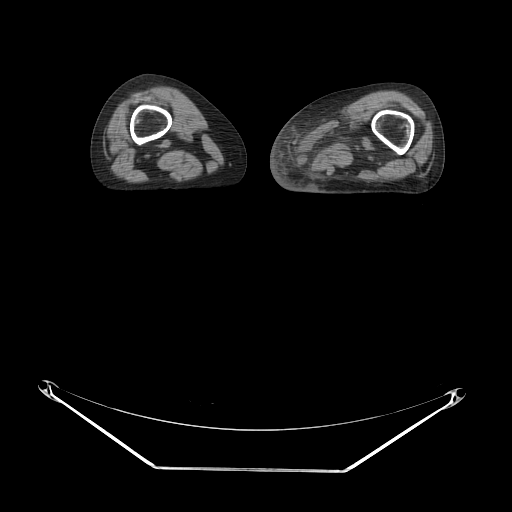
CT of an extremity soft-tissue mass (from a PET/CT study), one axial slice; position 5 of 91 along the scan axis; reconstruction kernel STANDARD; 140 kVp; soft-tissue window (W 400 / L 40 HU); 512 × 512 image matrix, field of view 500 × 500 mm. Female patient. Case-level facts recorded for this patient, not image findings: histological type: pleomorphic leiomyosarcoma; grade: high; site of the primary tumour: left thigh.
Annotated regions visible in this slice (expert contour drawn on MRI and transferred to this co-registered scan by the dataset authors):
- gross tumour volume including surrounding oedema: bounding box (x1, y1, x2, y2) in pixels: (304, 107, 382, 177)